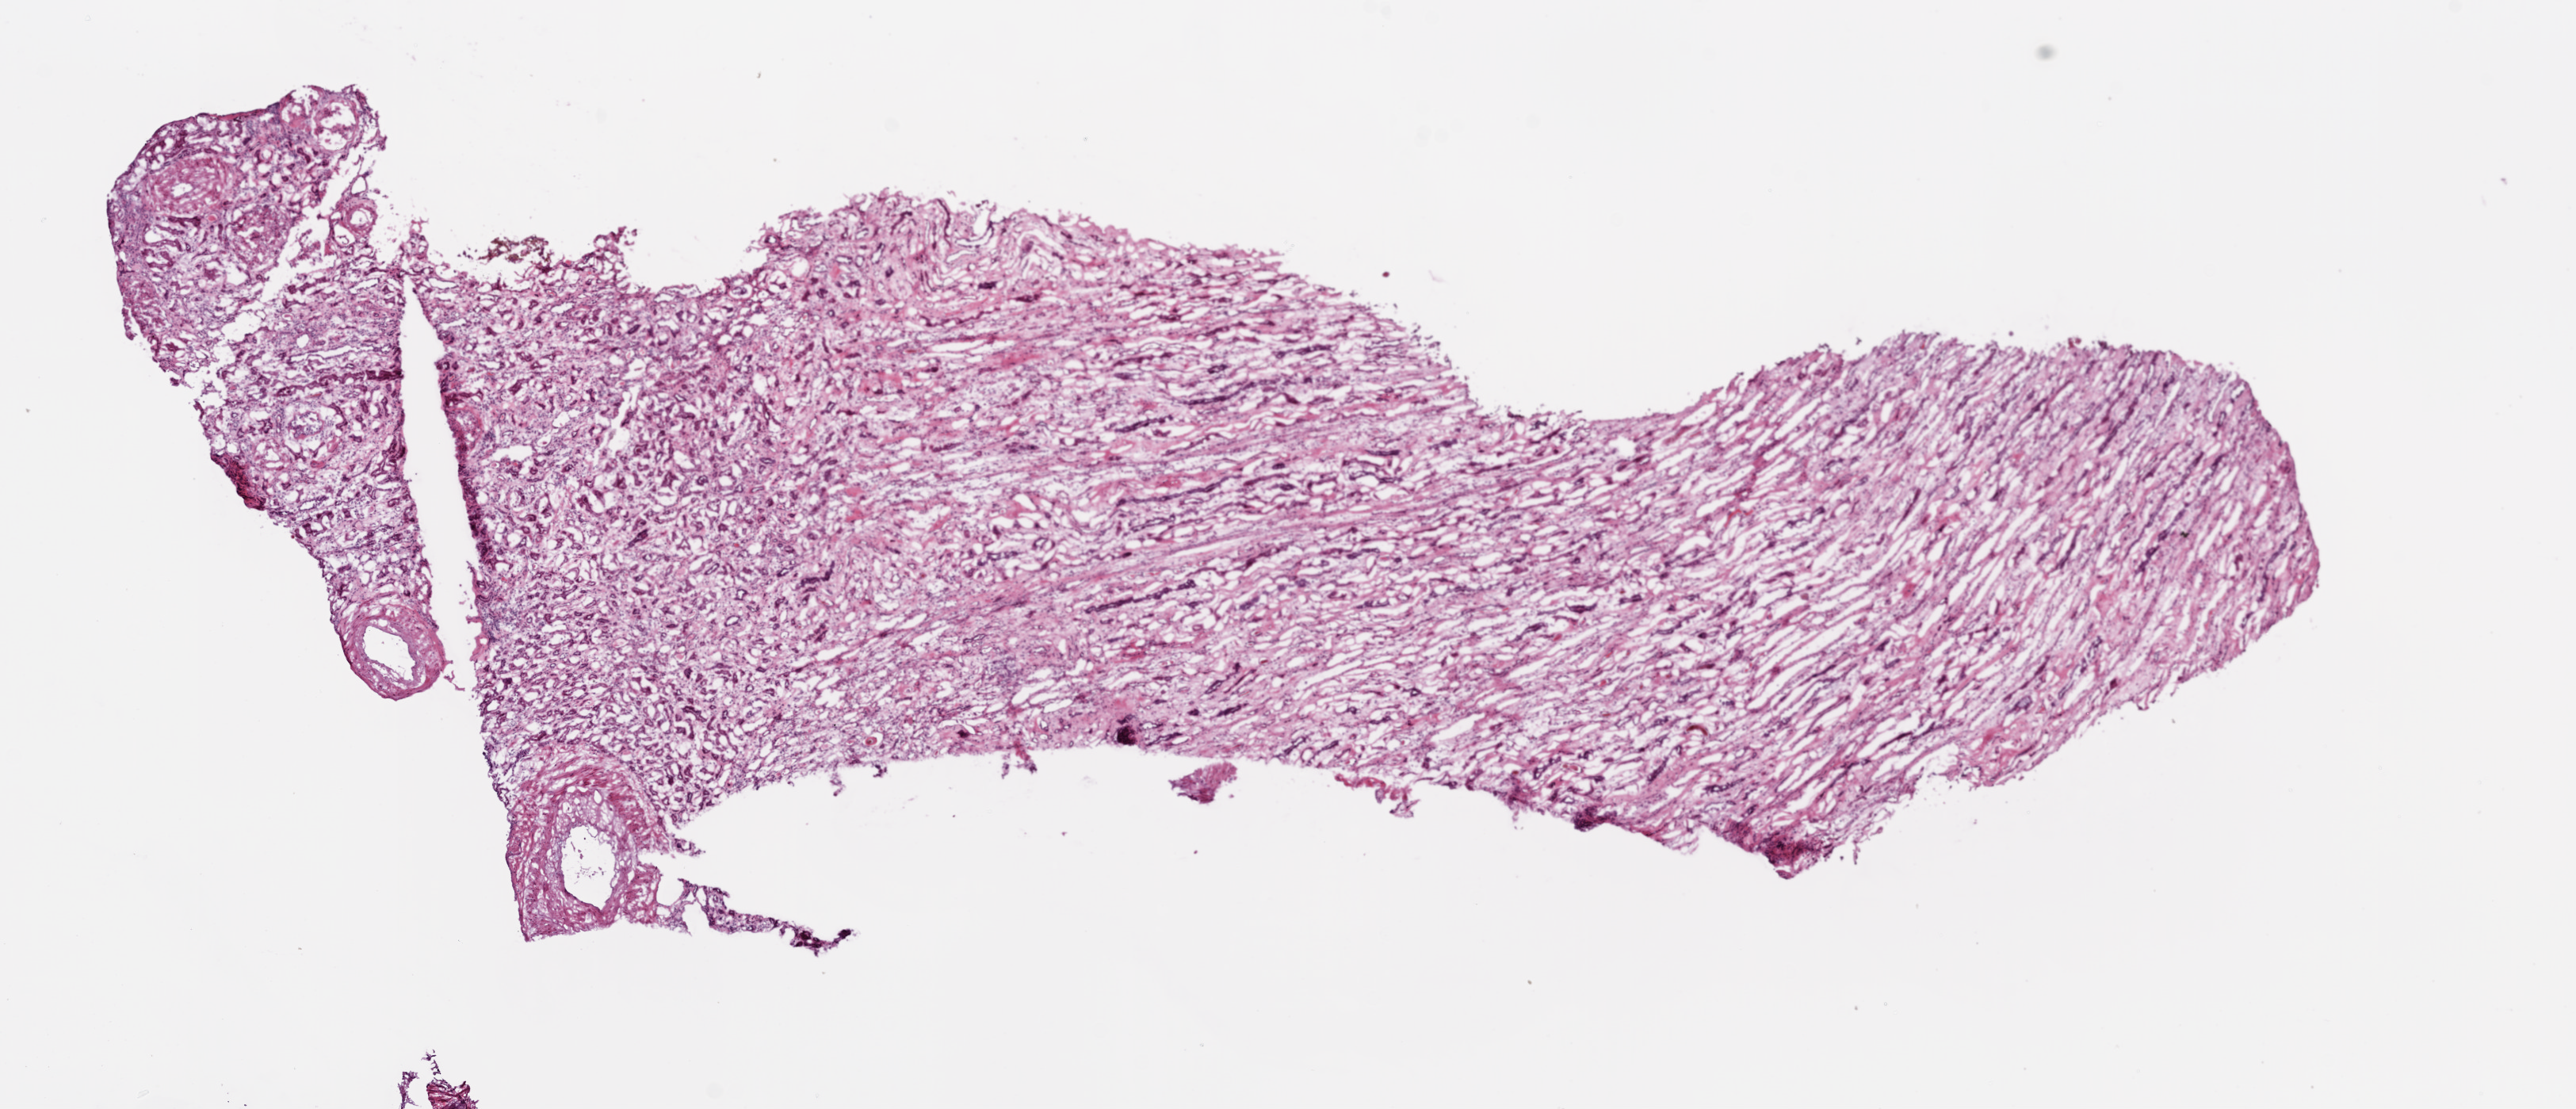
Digitized Hematoxylin and eosin (H&E) stained tissue section (whole slide), shown as a low-resolution overview of the whole scanned area (about 13.0 x 5.6 mm); frozen section from the bottom of the tissue portion; solid tissue normal (non-tumour tissue) sample from the kidney. Patient: male, age at initial diagnosis 63 years.
This section: solid tissue normal (non-tumour) sample from the same patient. Patient diagnosis: Clear cell adenocarcinoma, NOS.